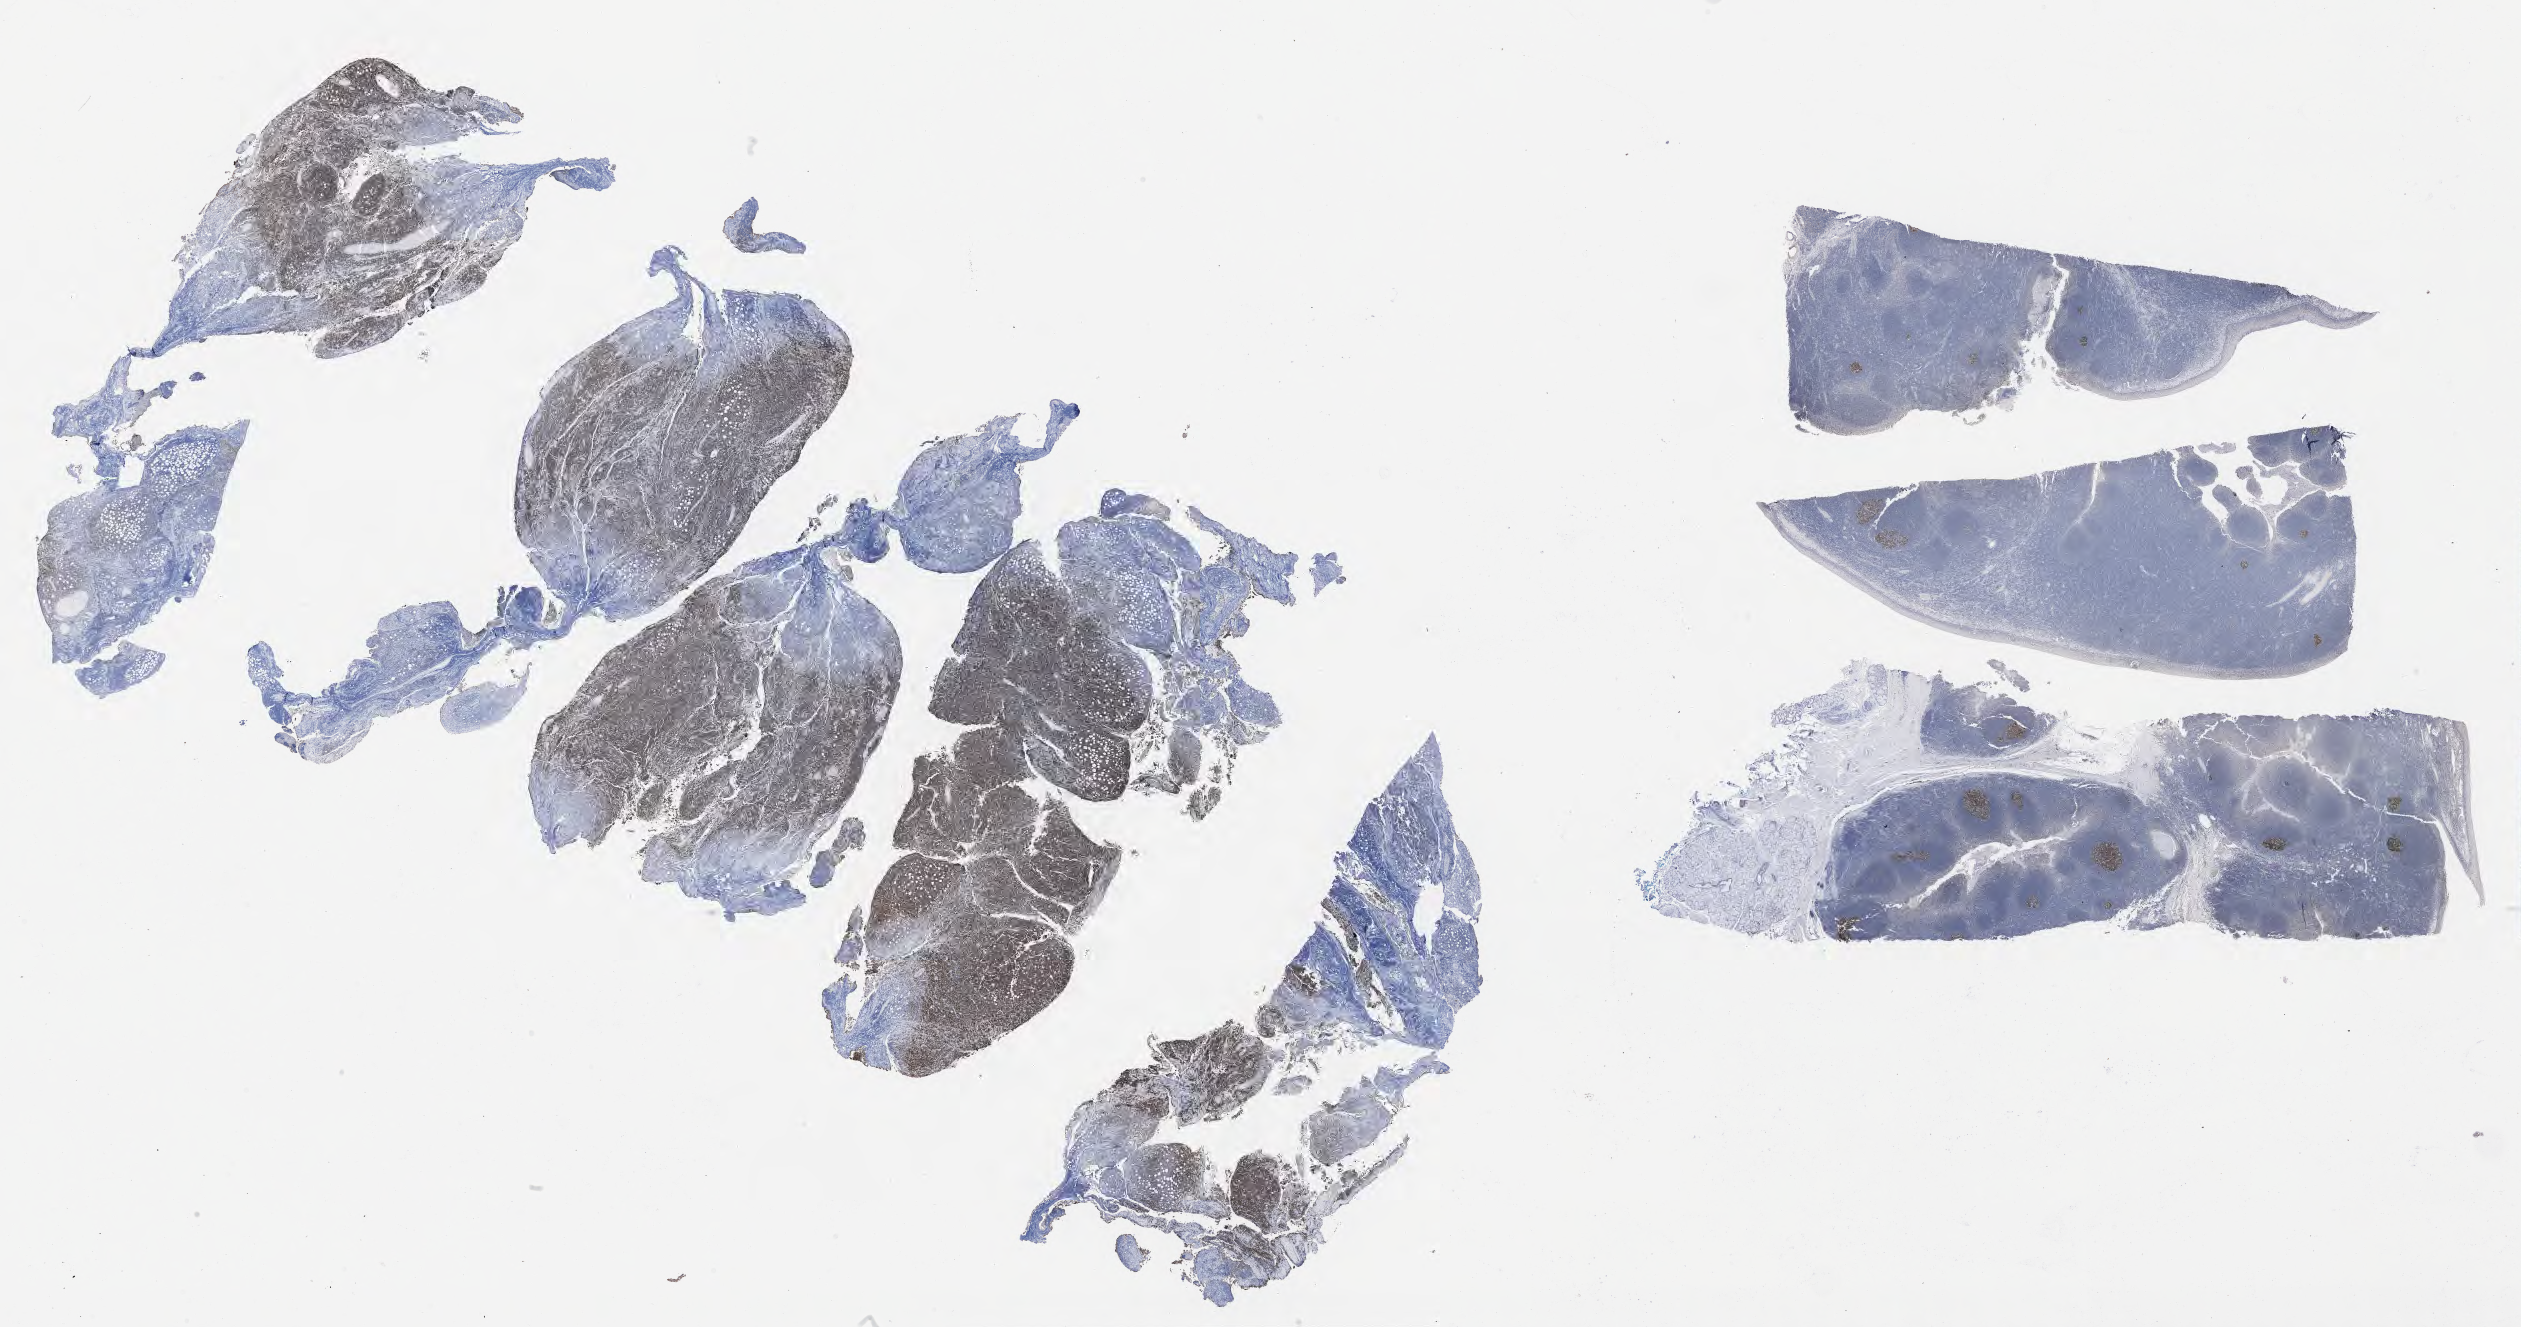
Immunohistochemistry (IHC) whole-slide image stained for BCL6, shown as a low-resolution overview of the whole scanned area (about 40.7 x 21.4 mm), tumor tissue, anatomic site: peritoneum. Male, age 8 years at initial diagnosis.
Histologic diagnosis: Burkitt lymphoma, NOS.